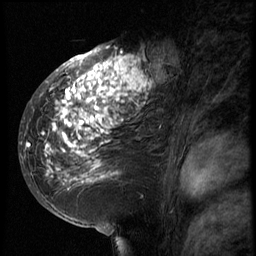
Breast MRI (dynamic contrast-enhanced), one sagittal slice; slice 39 of 66 in the series (ordered by position); 3 images stored at this slice position (order not interpretable as contrast timing); 1.5 T; TE 4.2 ms, TR 8.9 ms; 2.5 mm slice thickness; 256 × 256 image matrix, field of view 200 × 200 mm. Female patient, age 39 years. From the clinical record (not read from this slice): setting: breast cancer imaged before/during neoadjuvant chemotherapy; receptor status: HER2-positive.
Outlined on this slice (semi-automatically segmented with operator editing):
- analysis volume of interest (the breast-tissue region the enhancement analysis was run in; not a lesion): box from (x=29, y=44) to (x=166, y=196) px
- tumour enhancement mask (voxels above the 140 % enhancement threshold inside the analysis volume of interest): (x=29, y=46)–(x=165, y=183)